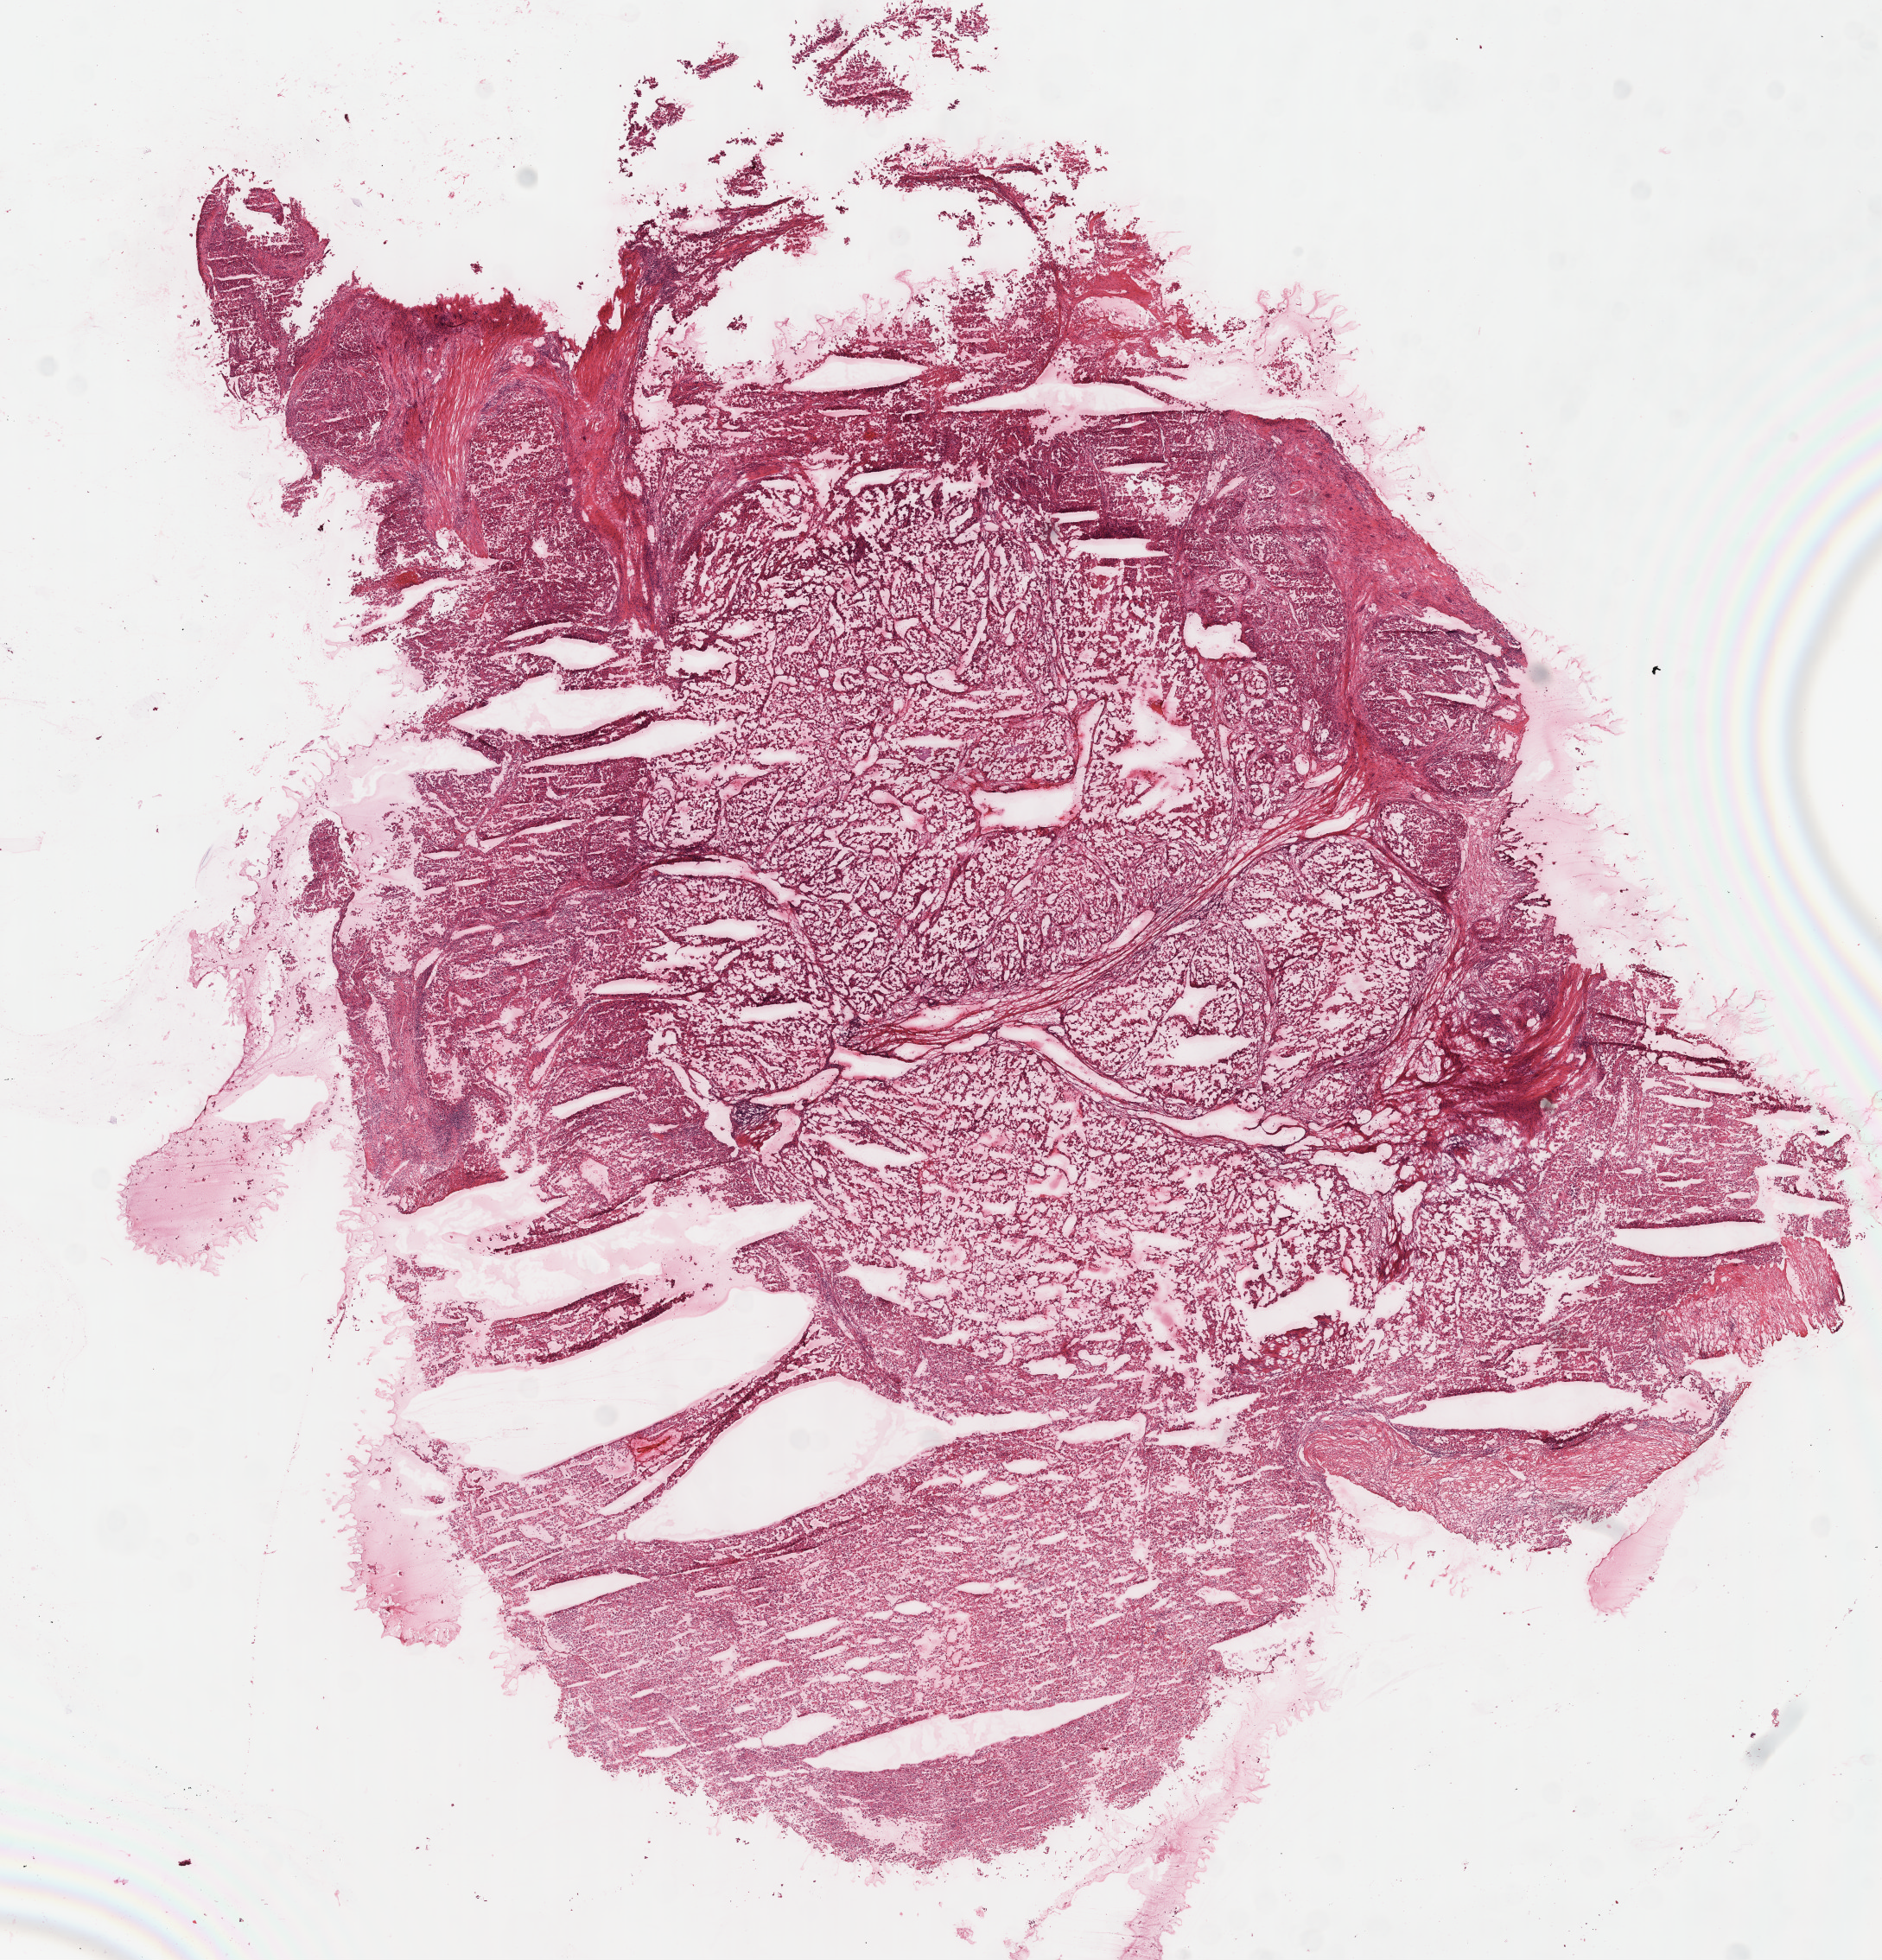
Hematoxylin and eosin (H&E) stained whole-slide image, a low-resolution overview of the entire scanned area, about 17.6 x 18.3 mm, frozen section from the top of the tissue portion, sample: primary tumour, kidney. Male patient; age at initial diagnosis 63 years. Histologic grade: G4 (undifferentiated). Composition of this section per pathologist review: tumour cells 80%, tumour nuclei 80%, normal cells 5%, stromal cells 15%, necrosis 0%.
* AJCC pathologic stage: III
* diagnosis: Clear cell adenocarcinoma, NOS